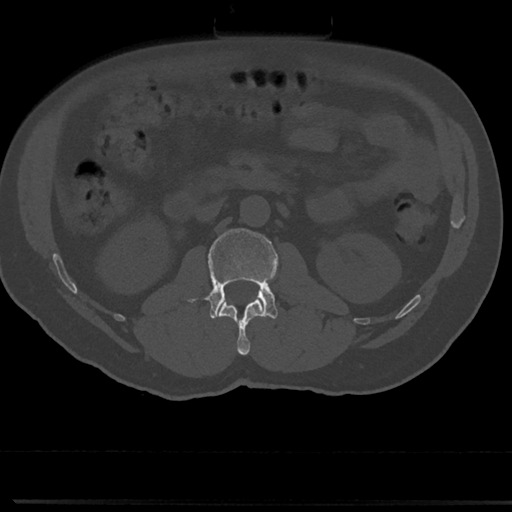
CT including the spine, one axial slice. Slice 38 of 817 in the series (ordered by position). Reconstruction kernel Br40s/3. Bone window (W 1800 / L 400 HU). 0.5 mm slice thickness. 512 × 512 image matrix, field of view 355 × 355 mm. Male patient, age 61 years. Case-level facts recorded for this patient, not image findings: primary cancer: prostate.
Outlined on this slice (semi-automatic segmentation, software-assisted and operator-edited):
- L1 vertebra: box from (x=219, y=299) to (x=263, y=355) px
- L2 vertebra: (x=207, y=228)–(x=277, y=318)